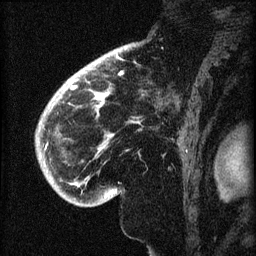
Breast MRI (dynamic contrast-enhanced), one sagittal slice. Position 50 of 60 along the scan axis. Dynamic contrast-enhanced series, image 2 of 3 at this slice position (ordered by acquisition). 1.5 T. TE 4.2 ms, TR 8.2 ms. 2 mm slice thickness. 256 × 256 image matrix, field of view 180 × 180 mm. Female patient, age 71 years.
Structures marked on this image (semi-automatically segmented with operator editing):
- analysis volume of interest (the breast-tissue region the enhancement analysis was run in; not a lesion): bounding box [x1, y1, x2, y2] px = [40, 72, 145, 196]
- tumour enhancement mask (voxels above the 70 % enhancement threshold inside the analysis volume of interest): [45, 73, 122, 150]